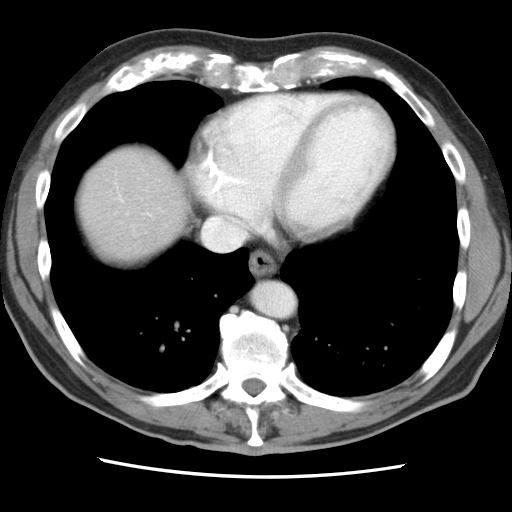
Contrast-enhanced abdominal CT, one axial slice. Position 80 of 83 along the scan axis. 120 kVp. Intravenous contrast given. Soft-tissue window (W 400 / L 40 HU). 5 mm slice thickness. 512 × 512 image matrix, field of view 321 × 321 mm. Male patient, age 69 years. Case-level facts recorded for this patient, not image findings: diagnosis: colorectal cancer liver metastases, imaged before liver resection.
Structures marked on this image (expert manual segmentation):
- hepatic veins: bounding box <120,199,246,251> (left, top, right, bottom; pixels)
- liver: <75,143,187,263>
- planned liver remnant (the part of the liver to remain after resection): <76,155,188,263>